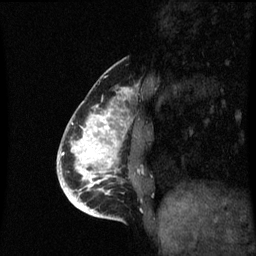
Breast MRI (dynamic contrast-enhanced), one sagittal slice. Dynamic contrast-enhanced series, image 2 of 3 at this slice position (ordered by acquisition). 1.5 T. TE 4.2 ms, TR 8.9 ms. 2 mm slice thickness. 256 × 256 image matrix, field of view 200 × 200 mm. Female patient, age 35 years. From the clinical record (not read from this slice): setting: breast cancer imaged before/during neoadjuvant chemotherapy; receptor status: HR-positive, HER2-negative.
Structures marked on this image (semi-automatic segmentation, software-assisted and operator-edited):
- analysis volume of interest (the breast-tissue region the enhancement analysis was run in; not a lesion): bounding box [x1, y1, x2, y2] px = [66, 106, 133, 215]
- tumour enhancement mask (voxels above the 70 % enhancement threshold inside the analysis volume of interest): [66, 108, 126, 215]